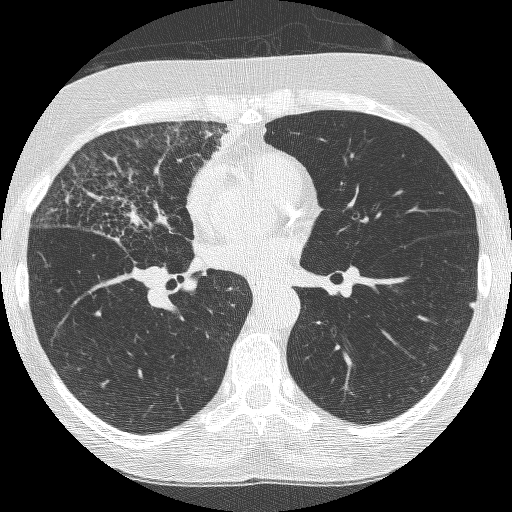
Axial slice from a low-dose chest CT screening exam, third screening round (two years after baseline), lung window (W 1500 / L -600 HU), 1.25 mm slice thickness, lung (sharp) reconstruction kernel (BONE). Female, age 64 years at enrolment.
- Expert reader's lesion annotation, bounding box [x1, y1, x2, y2] px = [53, 158, 200, 307].
- The exam's reader record, not a measurement of the box and not confirmed to be the same lesion: non-calcified nodule or mass ≥4 mm, right upper lobe, 49 × 43 mm, spiculated (stellate) margins, soft tissue attenuation, pre-existing on the prior screen: yes; interval growth: yes.
- Official screen result: positive, other.